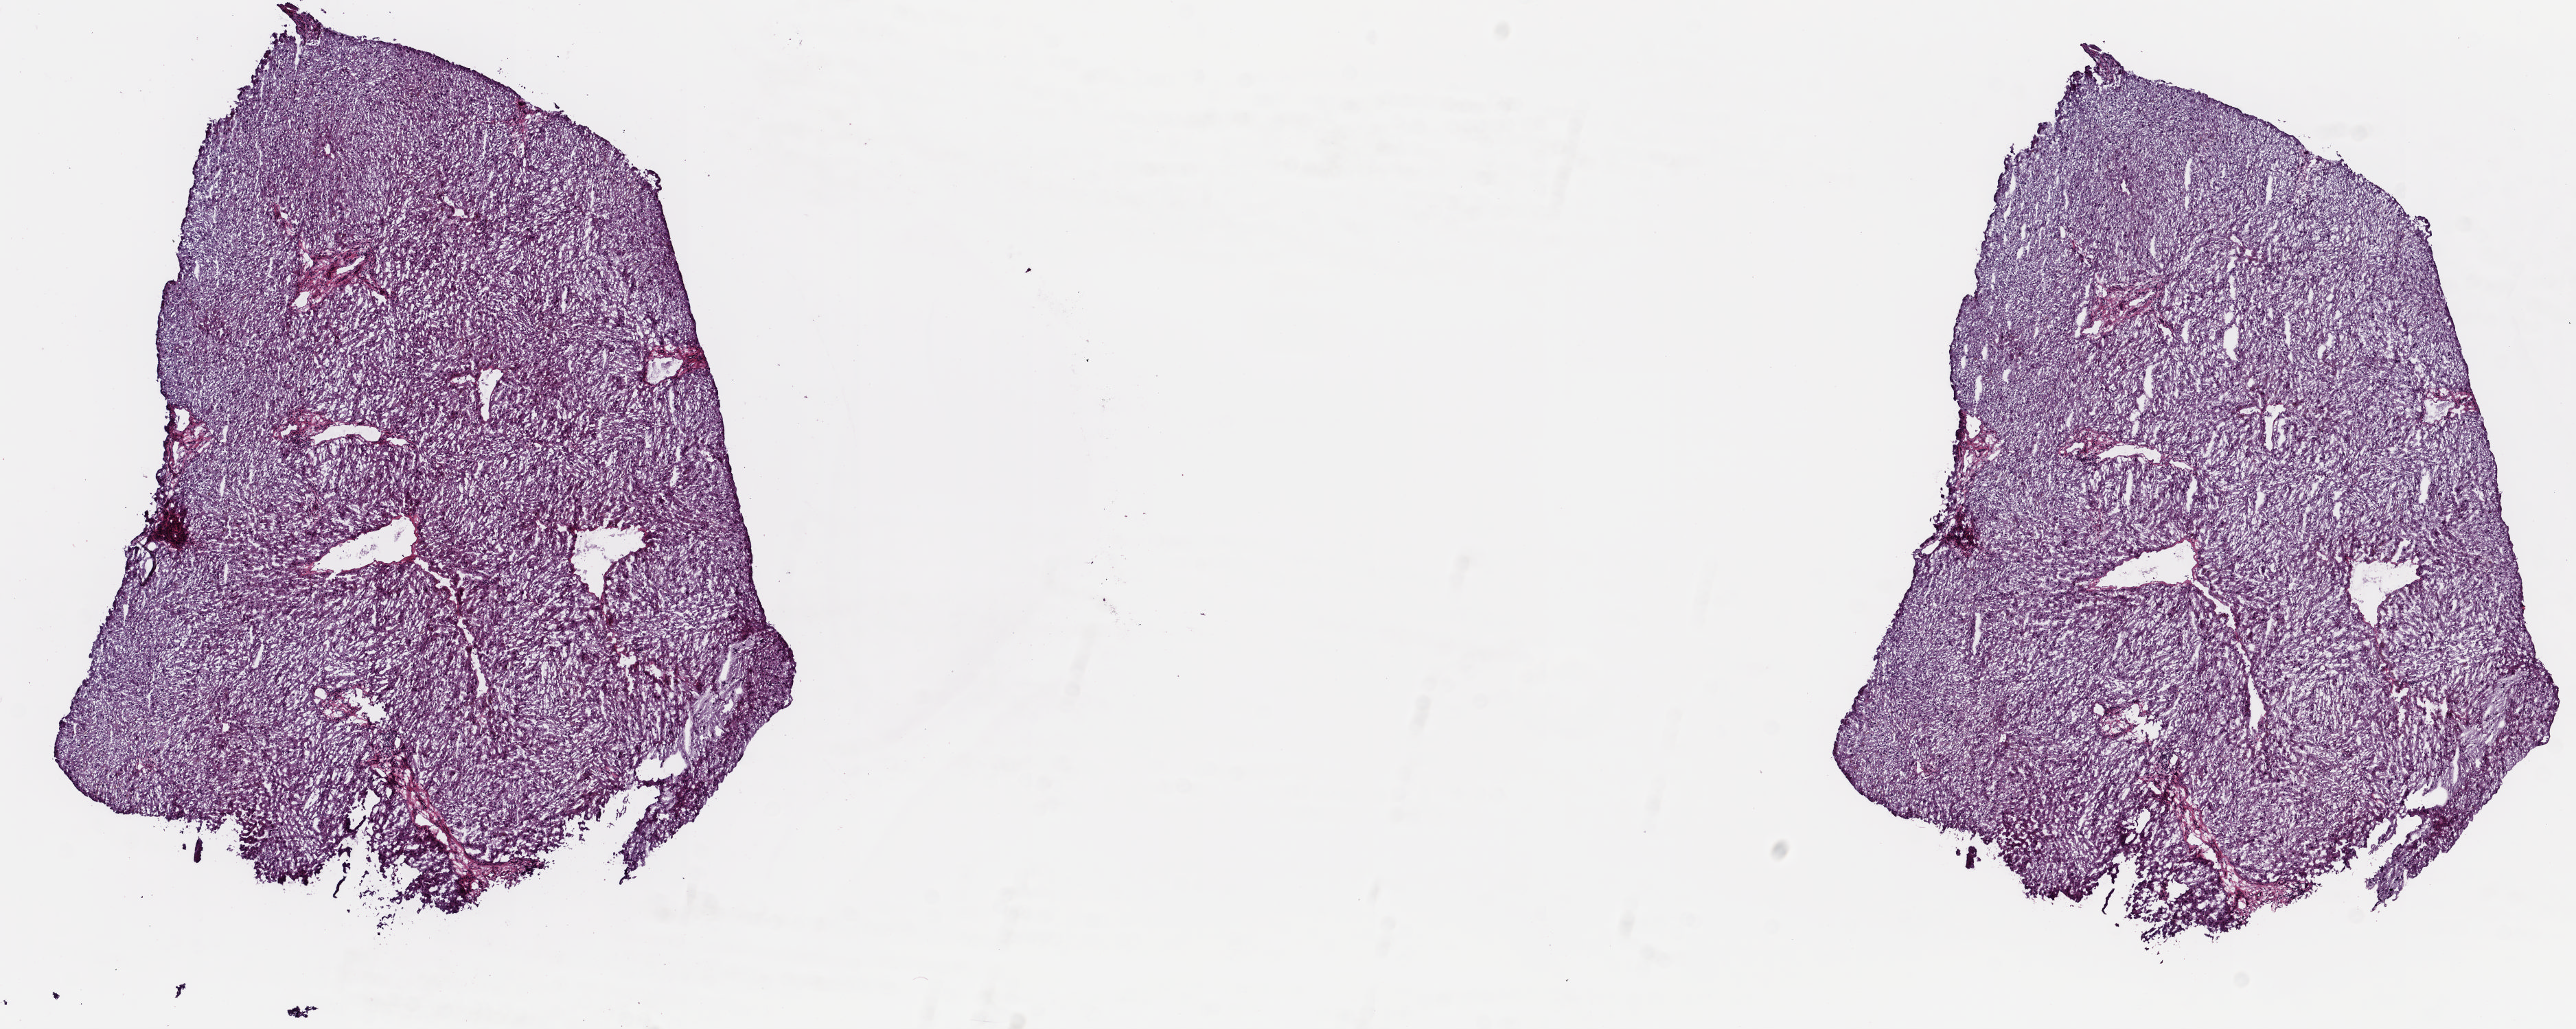
H&E-stained whole-slide image, low-resolution overview of the scanned area, about 14.9 x 5.9 mm (slide scanned at 20x); frozen section; solid tissue normal (non-tumour tissue) sample from the liver. Female, age 72 years at initial diagnosis. Slide review estimates, as recorded: tumour cells 0%, tumour nuclei 0%, normal cells 100%, stromal cells 0%, necrosis 0%. Inflammatory infiltration, as recorded: lymphocyte infiltration 0%, monocyte infiltration 0%, neutrophil infiltration 0%.
- this section: solid tissue normal sample (biorepository sample class)
- patient diagnosis: Hepatocellular carcinoma, NOS